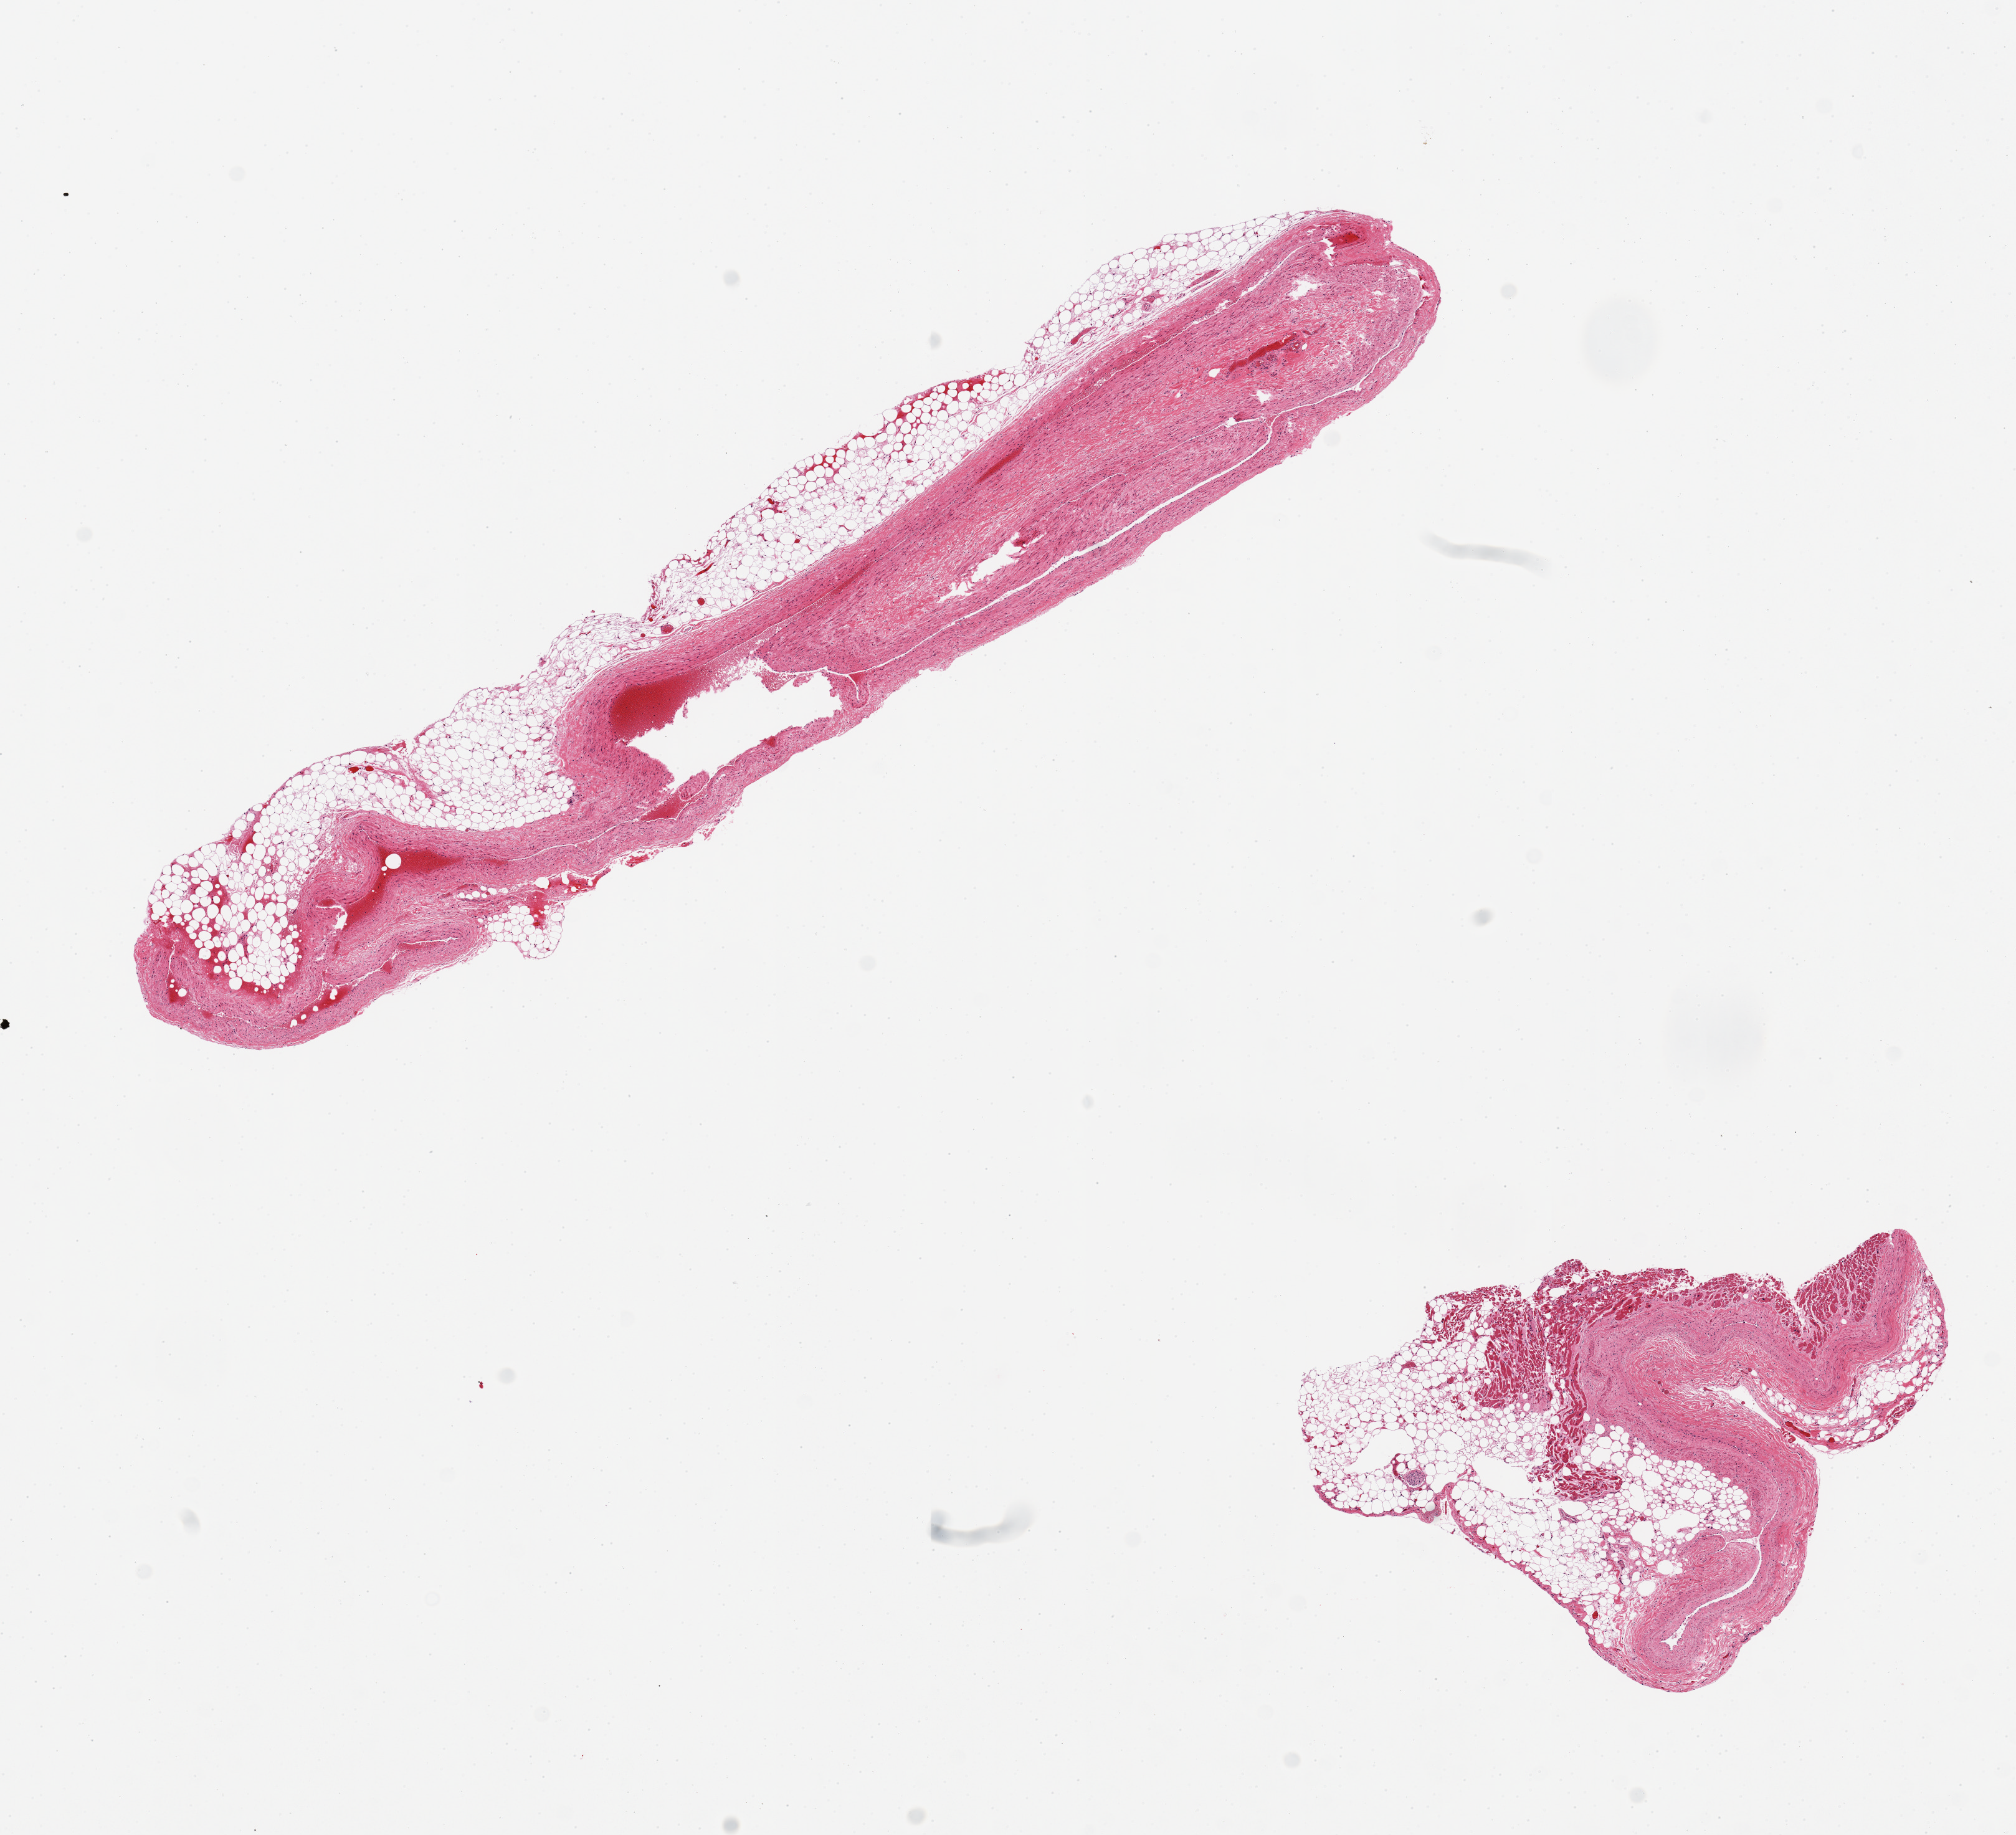
Whole-slide image, H&E stain, brightfield, low-resolution overview of the scanned area, about 12.8 x 11.6 mm (acquisition: 20x scan). PAXgene-fixed, paraffin-embedded tissue. Section of coronary artery (target tissue). Tissue donor sample.
* review note (as recorded): 2 pieces; 50% fat in 1, 30% fat in other